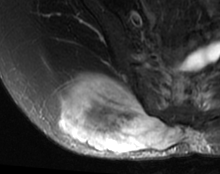
MRI of an extremity soft-tissue mass, one axial slice; position 34 of 63 along the scan axis; T2-weighted fat-saturated; MR volume resampled by the dataset authors to the PET/CT grid (not the native acquisition matrix); 220 × 174 image matrix, field of view 215 × 170 mm. Female patient. From the clinical record (not read from this slice): histological type: spindle cell suggestive of myxofibrosarcoma; grade: intermediate; site of the primary tumour: right buttock.
Annotated regions visible in this slice (expert contour drawn on MRI and transferred to this co-registered scan by the dataset authors):
- gross tumour volume (mass): bounding box [x1, y1, x2, y2] px = [58, 77, 183, 154]